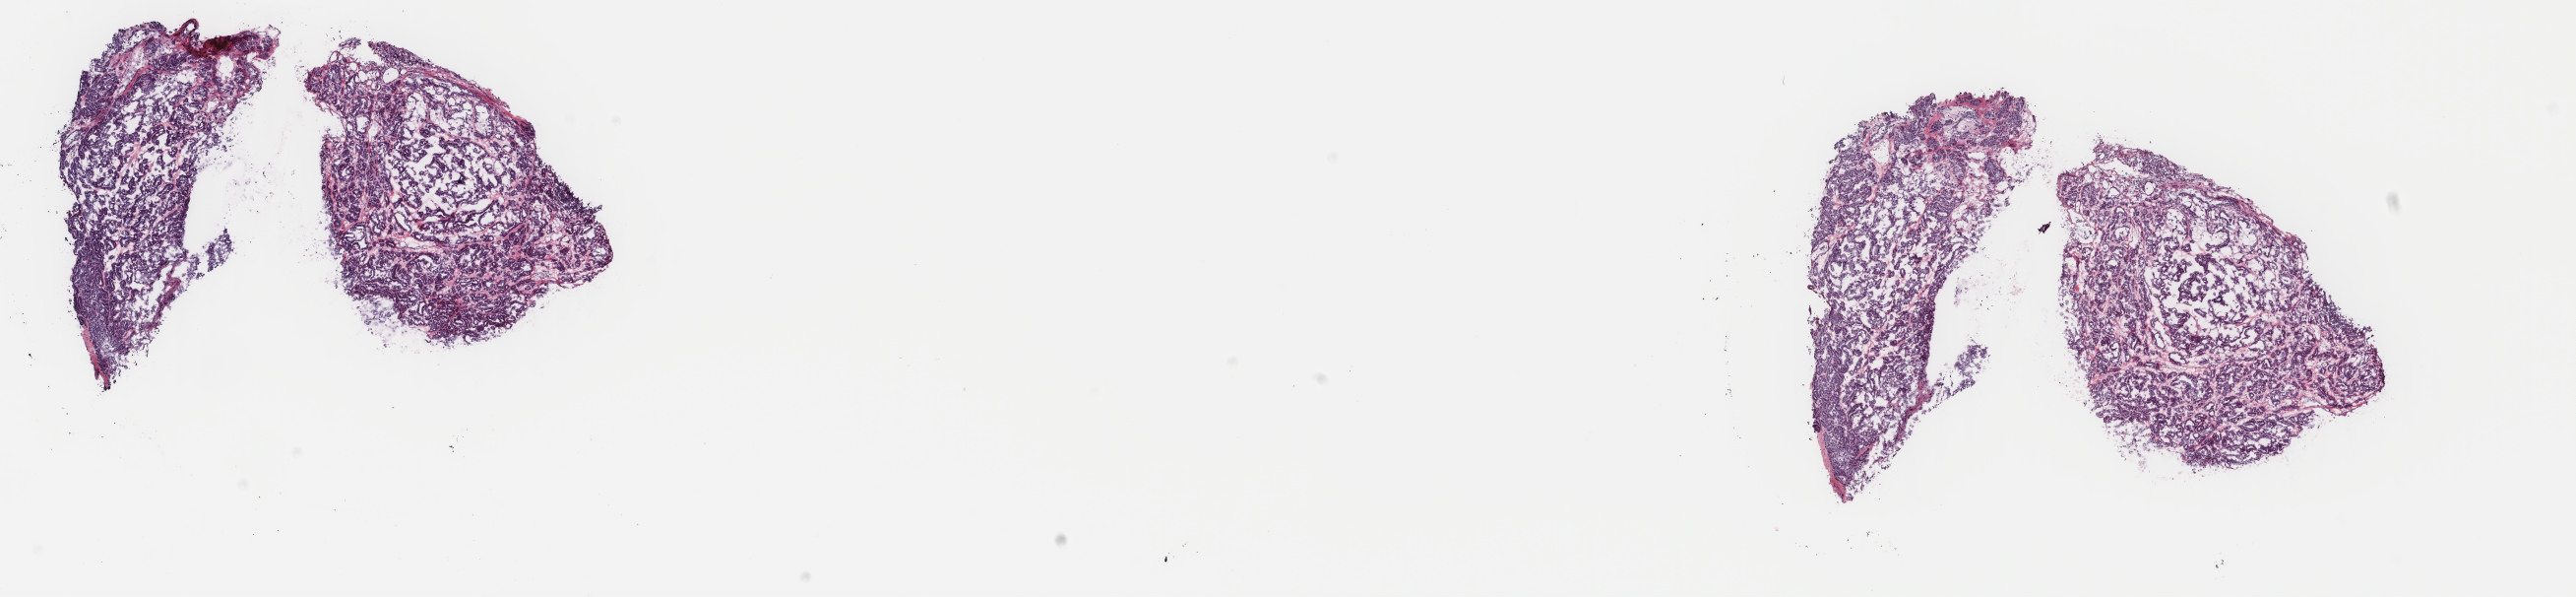
H&E-stained whole-slide image — low-resolution overview of the scanned area, about 20.8 x 4.8 mm (slide scanned at 40x), frozen section, thyroid, primary tumour sample. Female, age 48 years at initial diagnosis. Composition of this section per pathologist review: tumour cells 80%, tumour nuclei 100%, normal cells 0%, stromal cells 20%, necrosis 0%. Infiltration values recorded for this section: lymphocyte infiltration 1%, monocyte infiltration 1%, neutrophil infiltration 0%.
Lymph nodes positive (case pathology): 0 of 6 examined. Diagnosis: Papillary adenocarcinoma, NOS (thyroid gland). AJCC pathologic stage: III (7th edition).